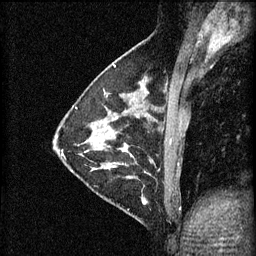
Breast MRI (dynamic contrast-enhanced), one sagittal slice; 3 images stored at this slice position (order not interpretable as contrast timing); 1.5 T; TE 4.2 ms, TR 11 ms; 256 × 256 image matrix. Female patient, age 29 years.
Structures marked on this image (semi-automatic segmentation, software-assisted and operator-edited):
- analysis volume of interest (the breast-tissue region the enhancement analysis was run in; not a lesion): bounding box (x1, y1, x2, y2) in pixels: (105, 172, 171, 227)
- tumour enhancement mask (voxels above the 70 % enhancement threshold inside the analysis volume of interest): (128, 172, 152, 205)